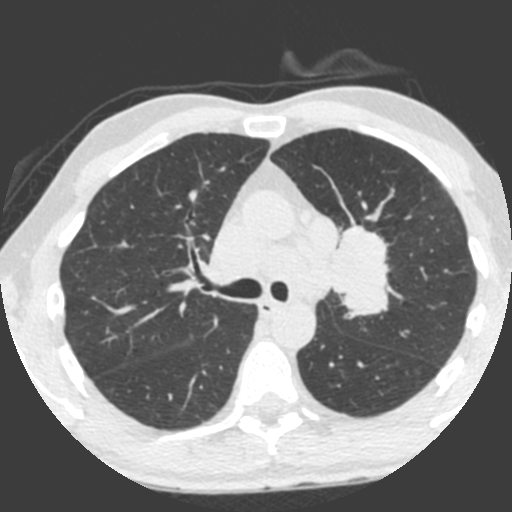
Low-dose screening chest CT, one axial slice. Slice 143 of 212 in the series (ordered by position). 120 kVp. Lung window (W 1500 / L -600 HU). 512 × 512 image matrix, field of view 315 × 315 mm.
Annotated regions visible in this slice (manually delineated by an expert):
- lesion 1 (tumor, upper lobe of left lung): bounding box <330,226,389,315> (left, top, right, bottom; pixels)